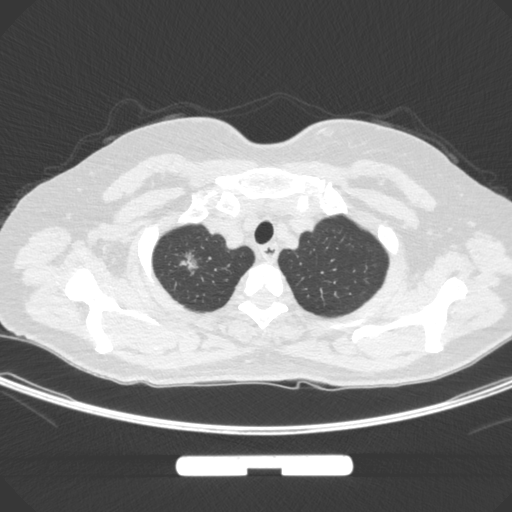
Chest CT, one axial slice. Slice 260 of 295 in the series (ordered by position). Lung window (W 1500 / L -600 HU). 1 mm slice thickness. 512 × 512 image matrix, field of view 369 × 369 mm. Female patient, age 58 years. Case-level facts recorded for this patient, not image findings: clinical TNM (as recorded): T1b N0 M0; histopathological grade: G2-3.
Outlined on this slice (rectangle marked by the reading radiologist):
- lung tumour (recorded histology: adenocarcinoma): bounding box <178,243,208,290> (left, top, right, bottom; pixels)